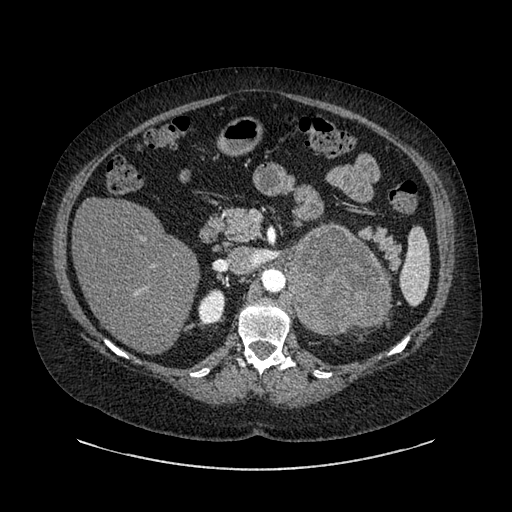
Contrast-enhanced abdominal CT, one axial slice; position 551 of 769 along the scan axis; reconstruction kernel SOFT; 120 kVp; soft-tissue window (W 400 / L 40 HU); 0.62 mm slice thickness; 512 × 512 image matrix. Female patient, age 61 years. Case-level facts recorded for this patient, not image findings: diagnosis: adrenocortical carcinoma; tumour side: left adrenal; tumour size at pathology: 13 cm; Ki-67 index: 79 %; stage (as recorded): 2.
Outlined on this slice (semi-automatic segmentation, software-assisted and operator-edited):
- mass: bounding box (x1, y1, x2, y2) in pixels: (289, 226, 388, 335)